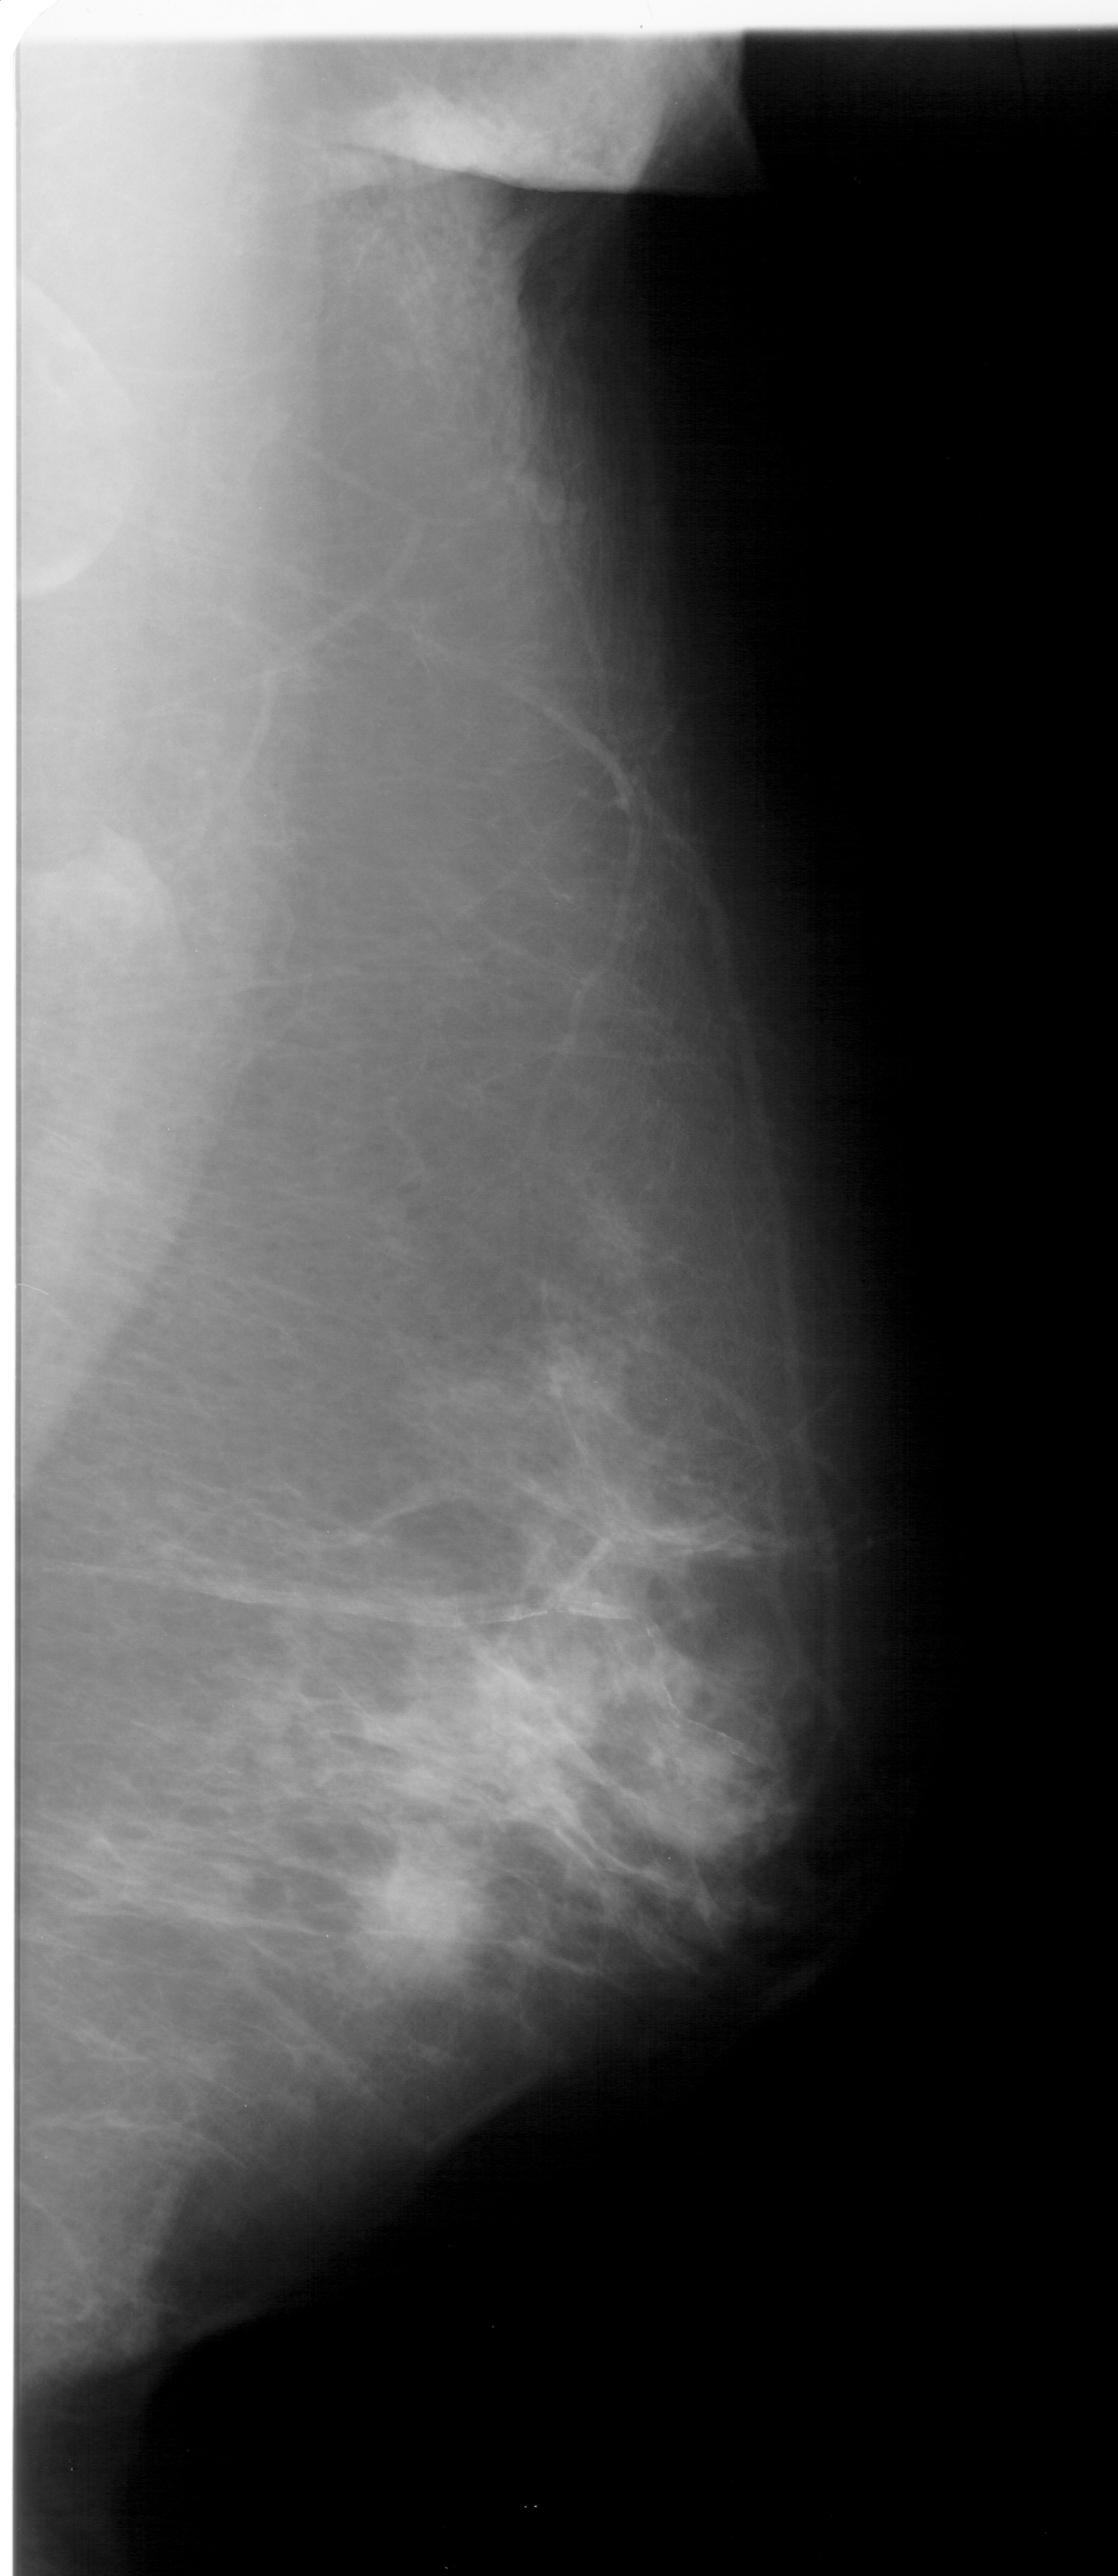
Scanned film-screen mammogram; right breast; mediolateral oblique (MLO) view; BI-RADS breast density category 3 (scale 1–4); 1118 × 2576 image matrix.
Expert-marked regions of interest on this image (one box per marked abnormality):
- calcifications, morphology pleomorphic, distribution clustered; BI-RADS assessment category 5; subtlety rating 4 on a 1 (subtle) to 5 (obvious) scale; pathology (as recorded): malignant: bounding box [x1, y1, x2, y2] px = [257, 1761, 568, 2034]